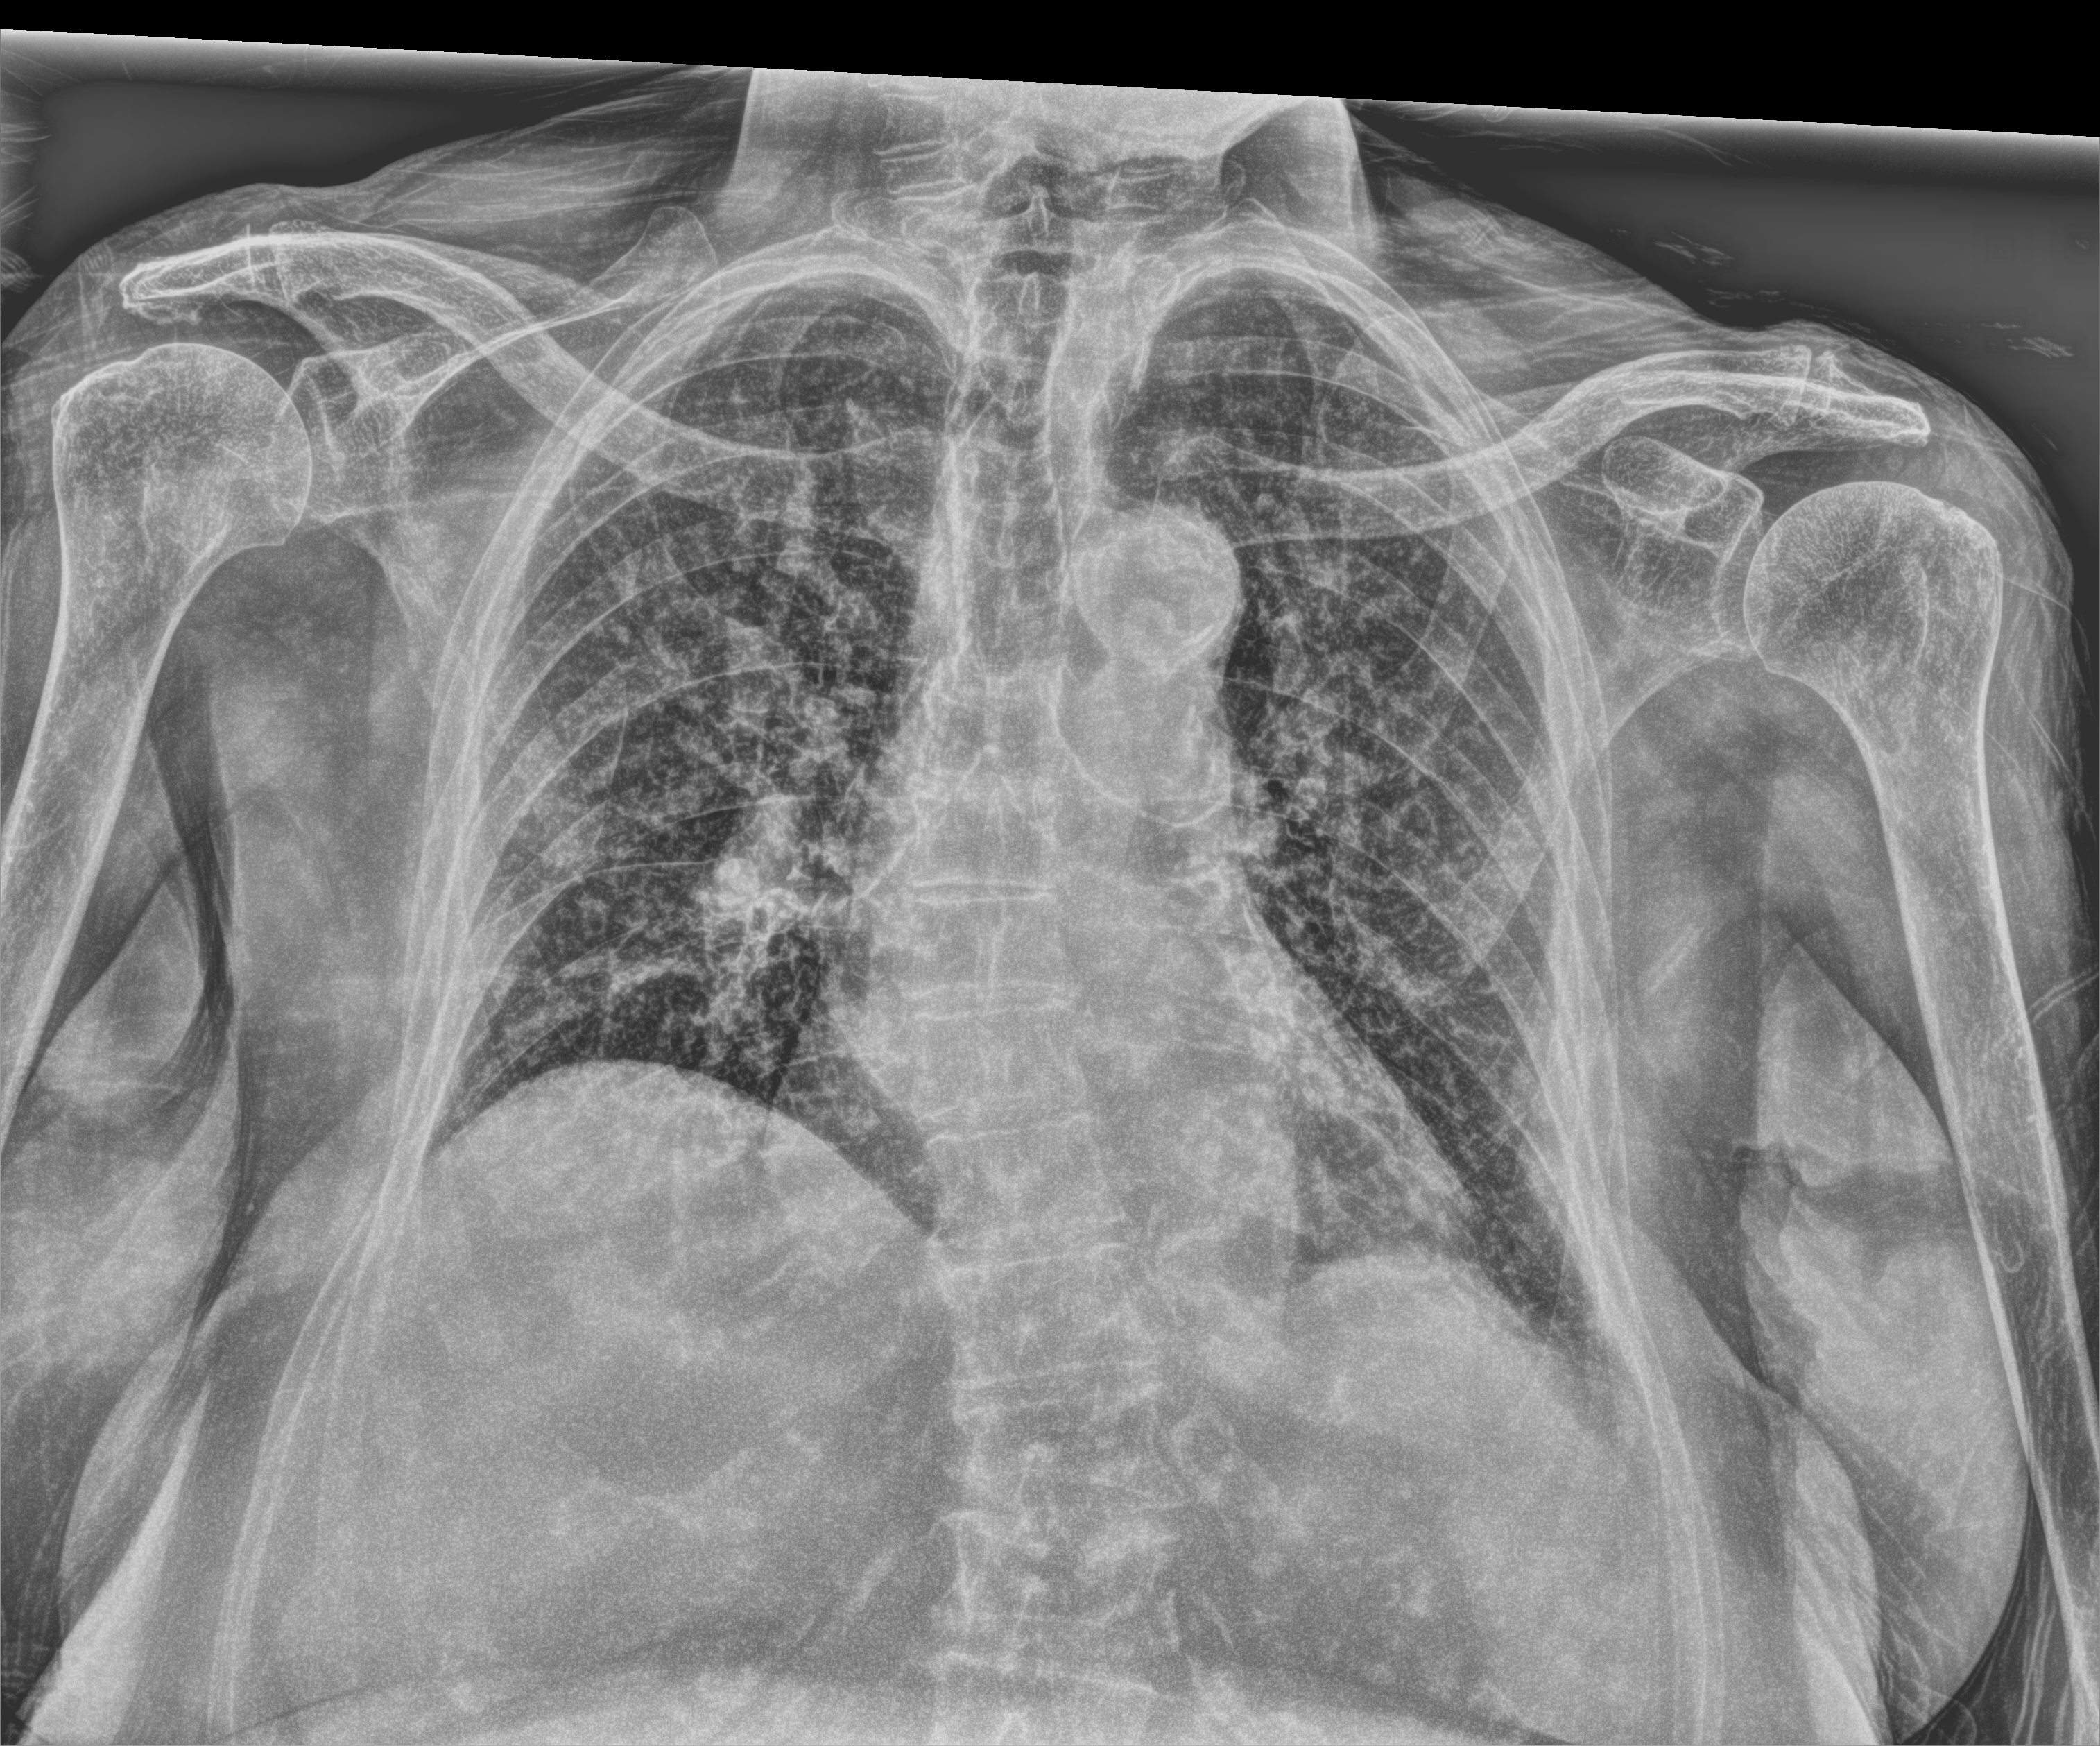
Portable chest radiograph; anteroposterior (AP) projection. Patient hospitalised with COVID-19; female, aged 75–90 years.
Admission-level facts for this patient (not findings on this image; timing relative to this image not recorded): COPD (admission record): no; admitted to intensive care during this hospital stay: no; length of hospital stay: 10 days.